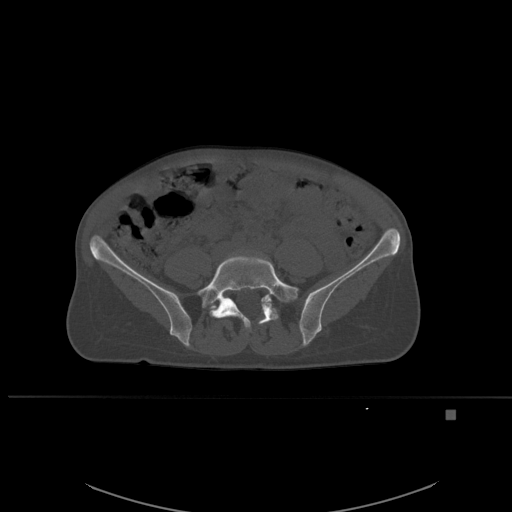
CT including the spine, one axial slice. Bone window (W 1800 / L 400 HU). 512 × 512 image matrix. Patient: female, 45 years. Case-level facts recorded for this patient, not image findings: primary cancer: lung.
Annotated regions visible in this slice (semi-automatically segmented with operator editing):
- L5 vertebra: bounding box (x1, y1, x2, y2) in pixels: (196, 253, 299, 332)